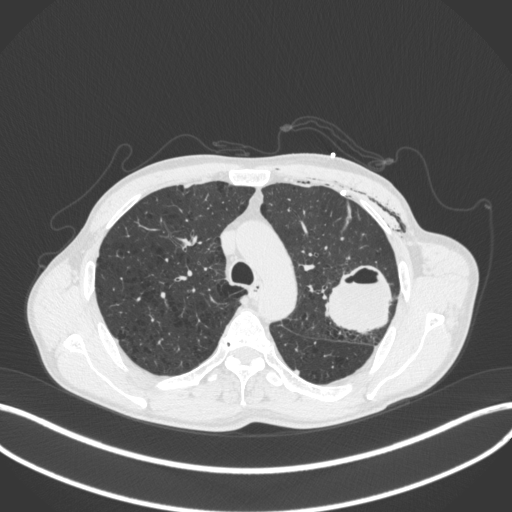
Chest CT, one axial slice. Position 288 of 416 along the scan axis. 120 kVp. Lung window (W 1500 / L -600 HU). 1 mm slice thickness. 512 × 512 image matrix, field of view 400 × 400 mm. Patient: male, 58 years. Case-level facts recorded for this patient, not image findings: clinical TNM (as recorded): T3 N0 M0.
Annotated regions visible in this slice (rectangle marked by the reading radiologist):
- lung tumour (recorded histology: adenocarcinoma): bounding box (x1, y1, x2, y2) in pixels: (325, 263, 398, 340)